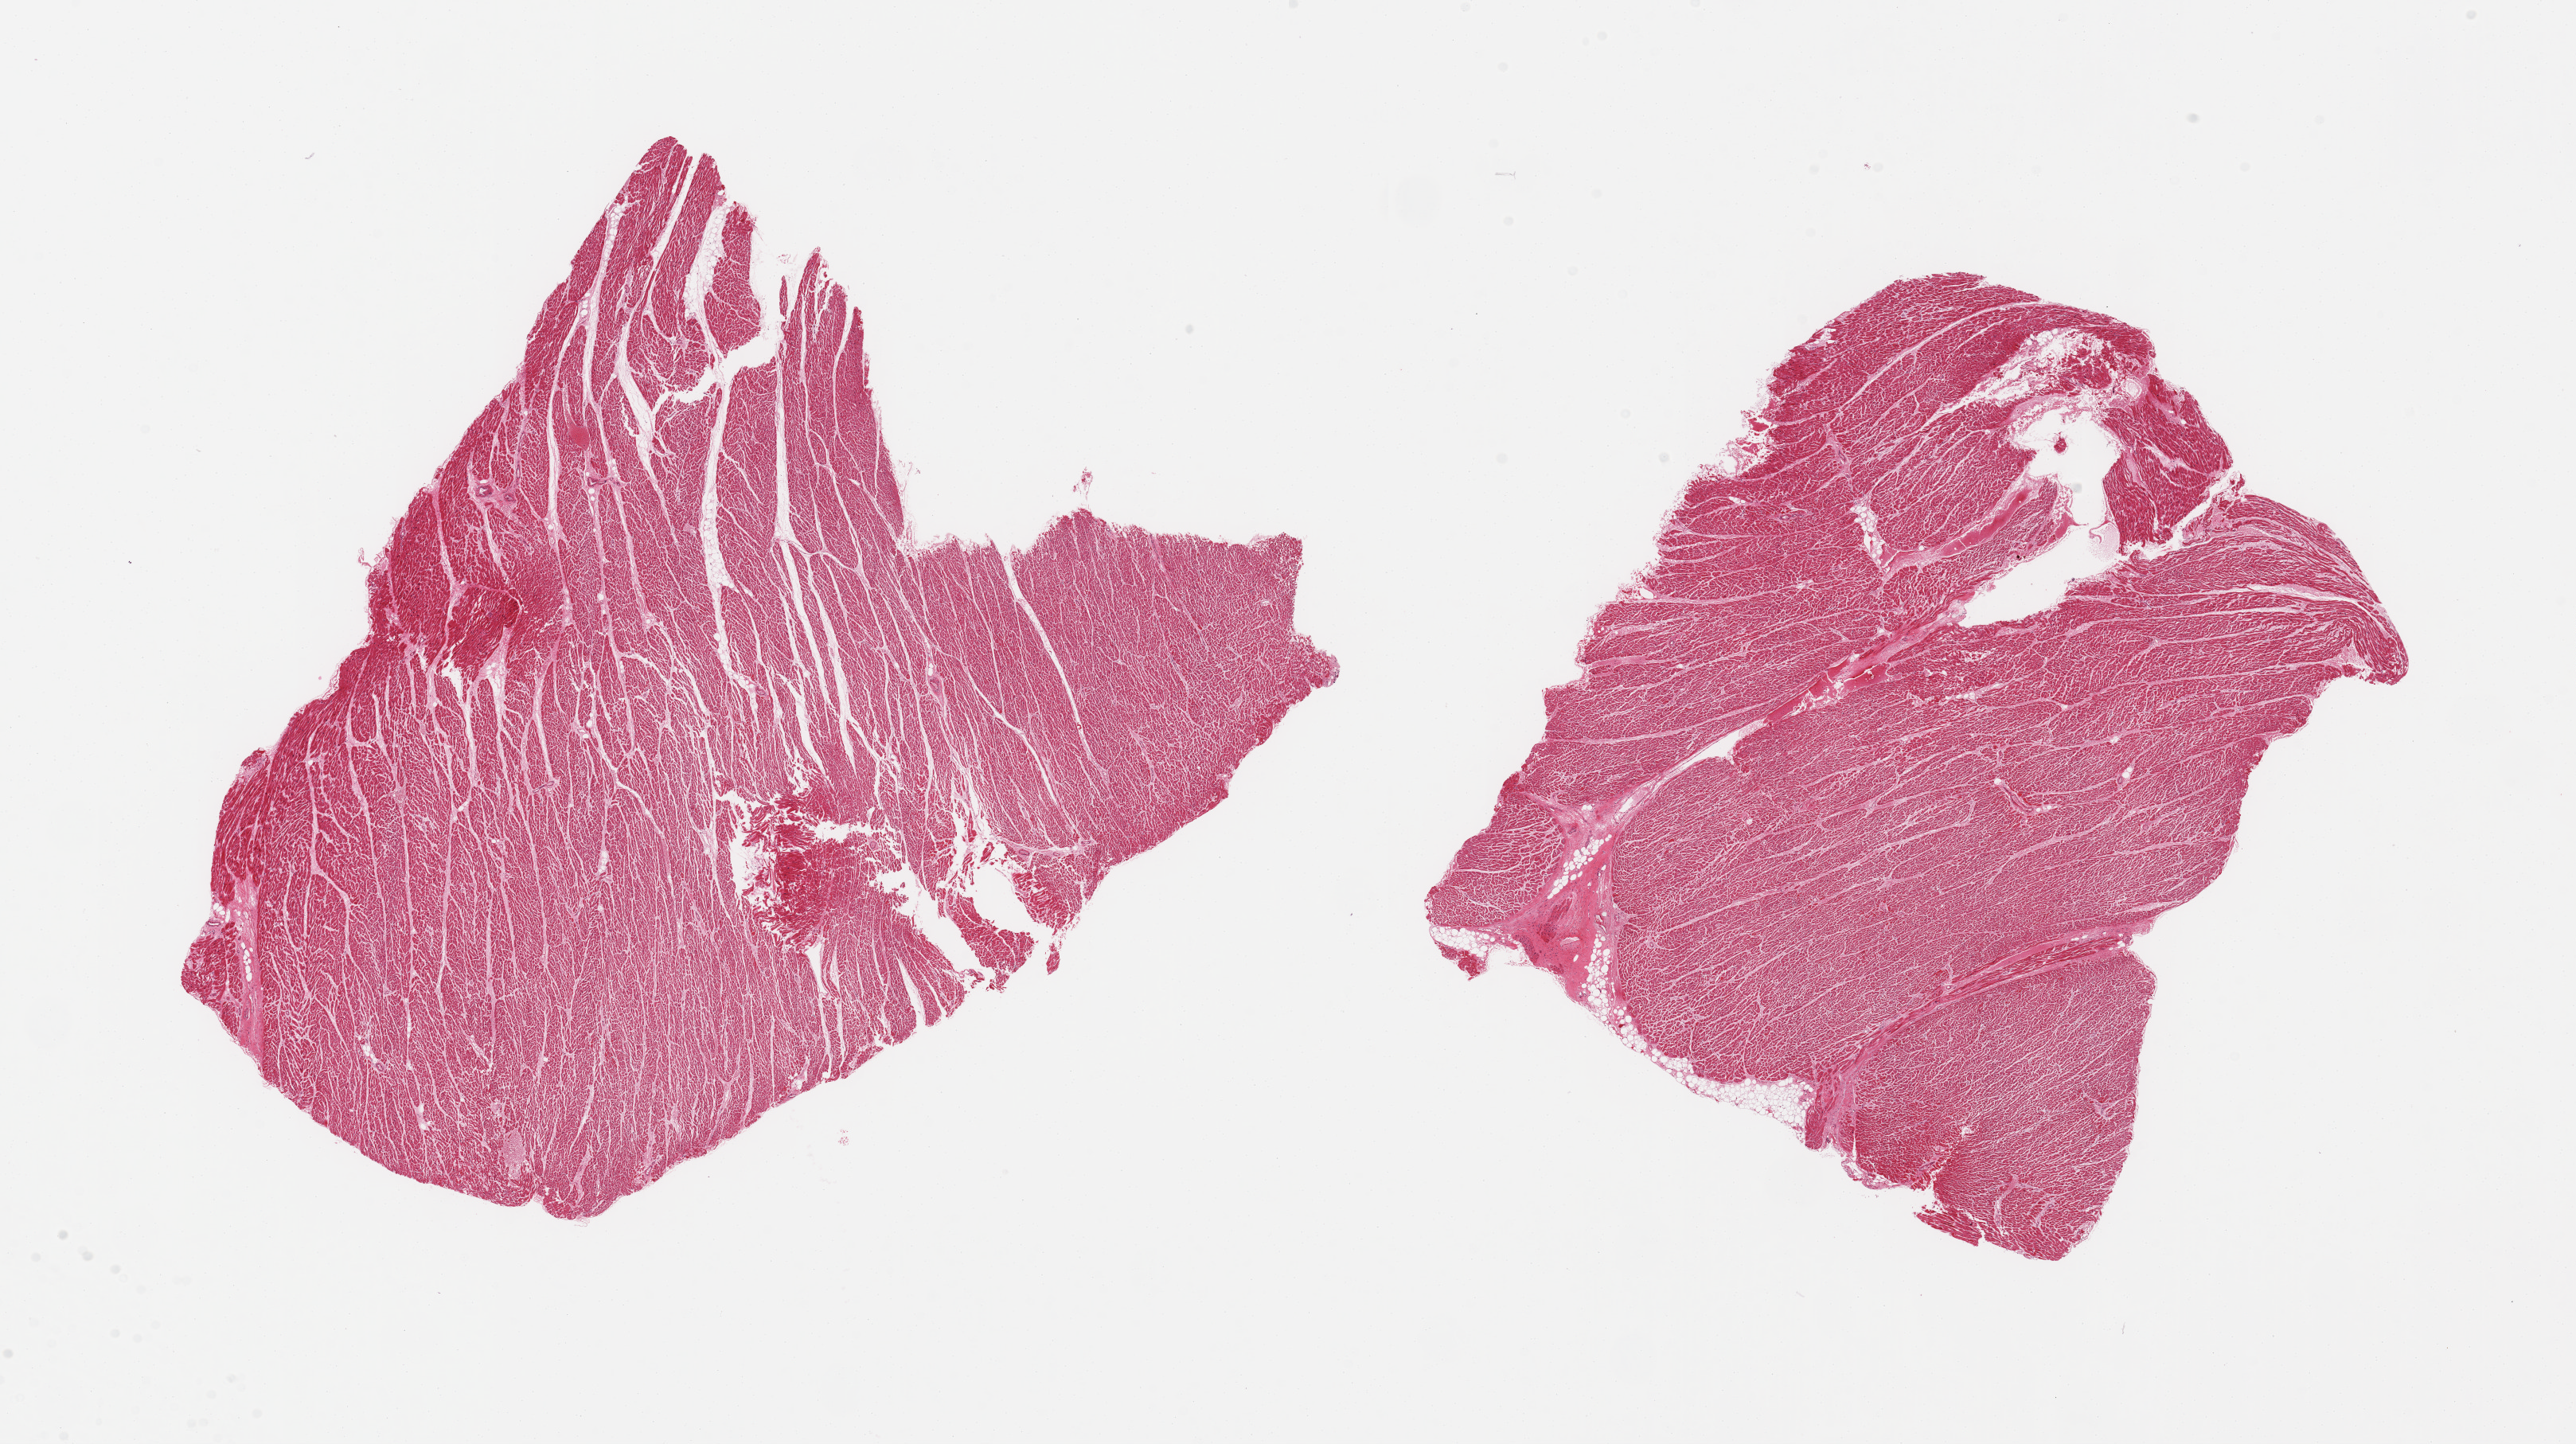
H&E whole-slide image, brightfield, shown as a low-resolution overview of the whole scanned area (about 25.6 x 14.3 mm); PAXgene-fixed, paraffin-embedded tissue; target tissue: heart; donor tissue sample. Male donor.
• pathologist's review note for this sample: 2 pieces, moderate interstitial fibrosis,/chronic ischemic changes